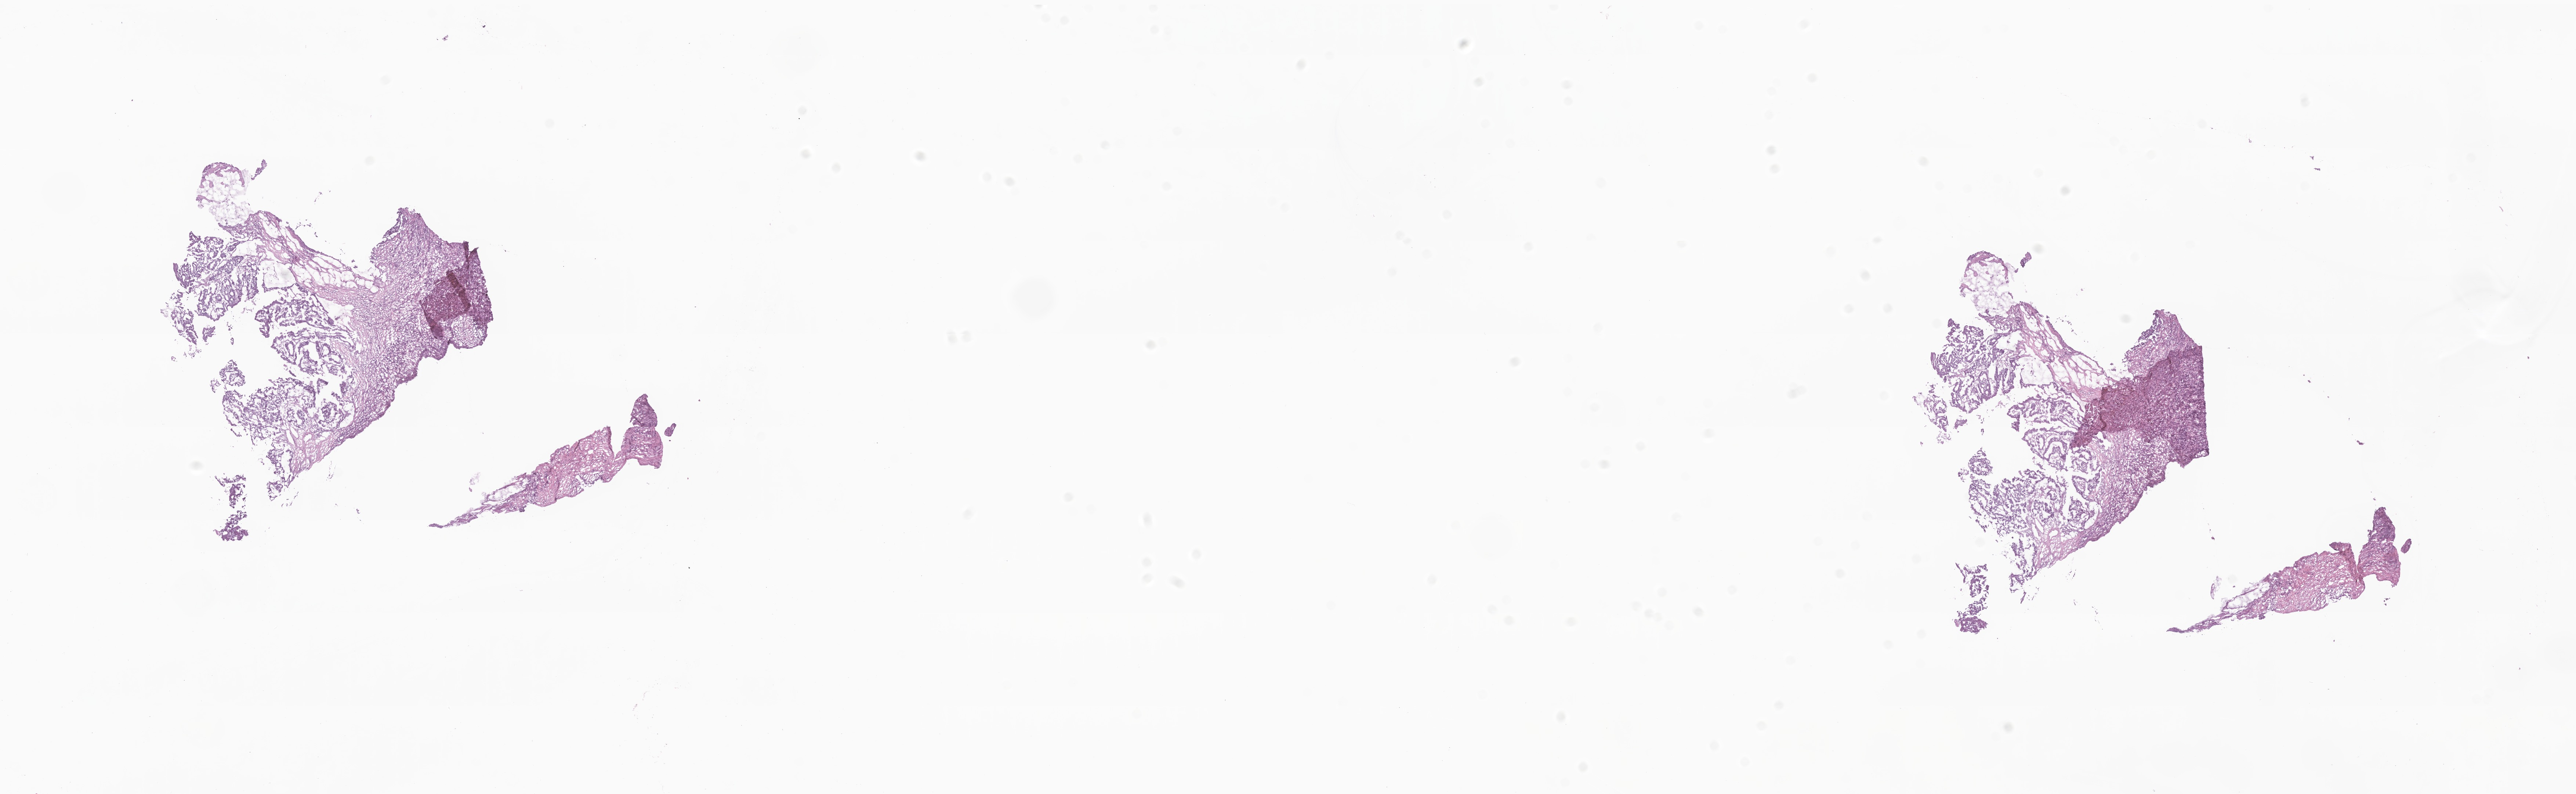
Digitized haematoxylin and eosin-stained section — a low-resolution overview of the entire scanned area, about 29.6 x 9.1 mm. Cryosection. Metastatic tumor tissue, resected from liver. Male patient; age at initial diagnosis 84 years. Slide review estimates, as recorded: tumor cells 80%, tumor nuclei 80%, stromal cells 19%, necrosis 1%, normal cells 0%. Infiltration values recorded for this section: lymphocyte infiltration 3%, monocyte infiltration 4%, neutrophil infiltration 7%.
* patient diagnosis (primary): Adenocarcinoma, NOS